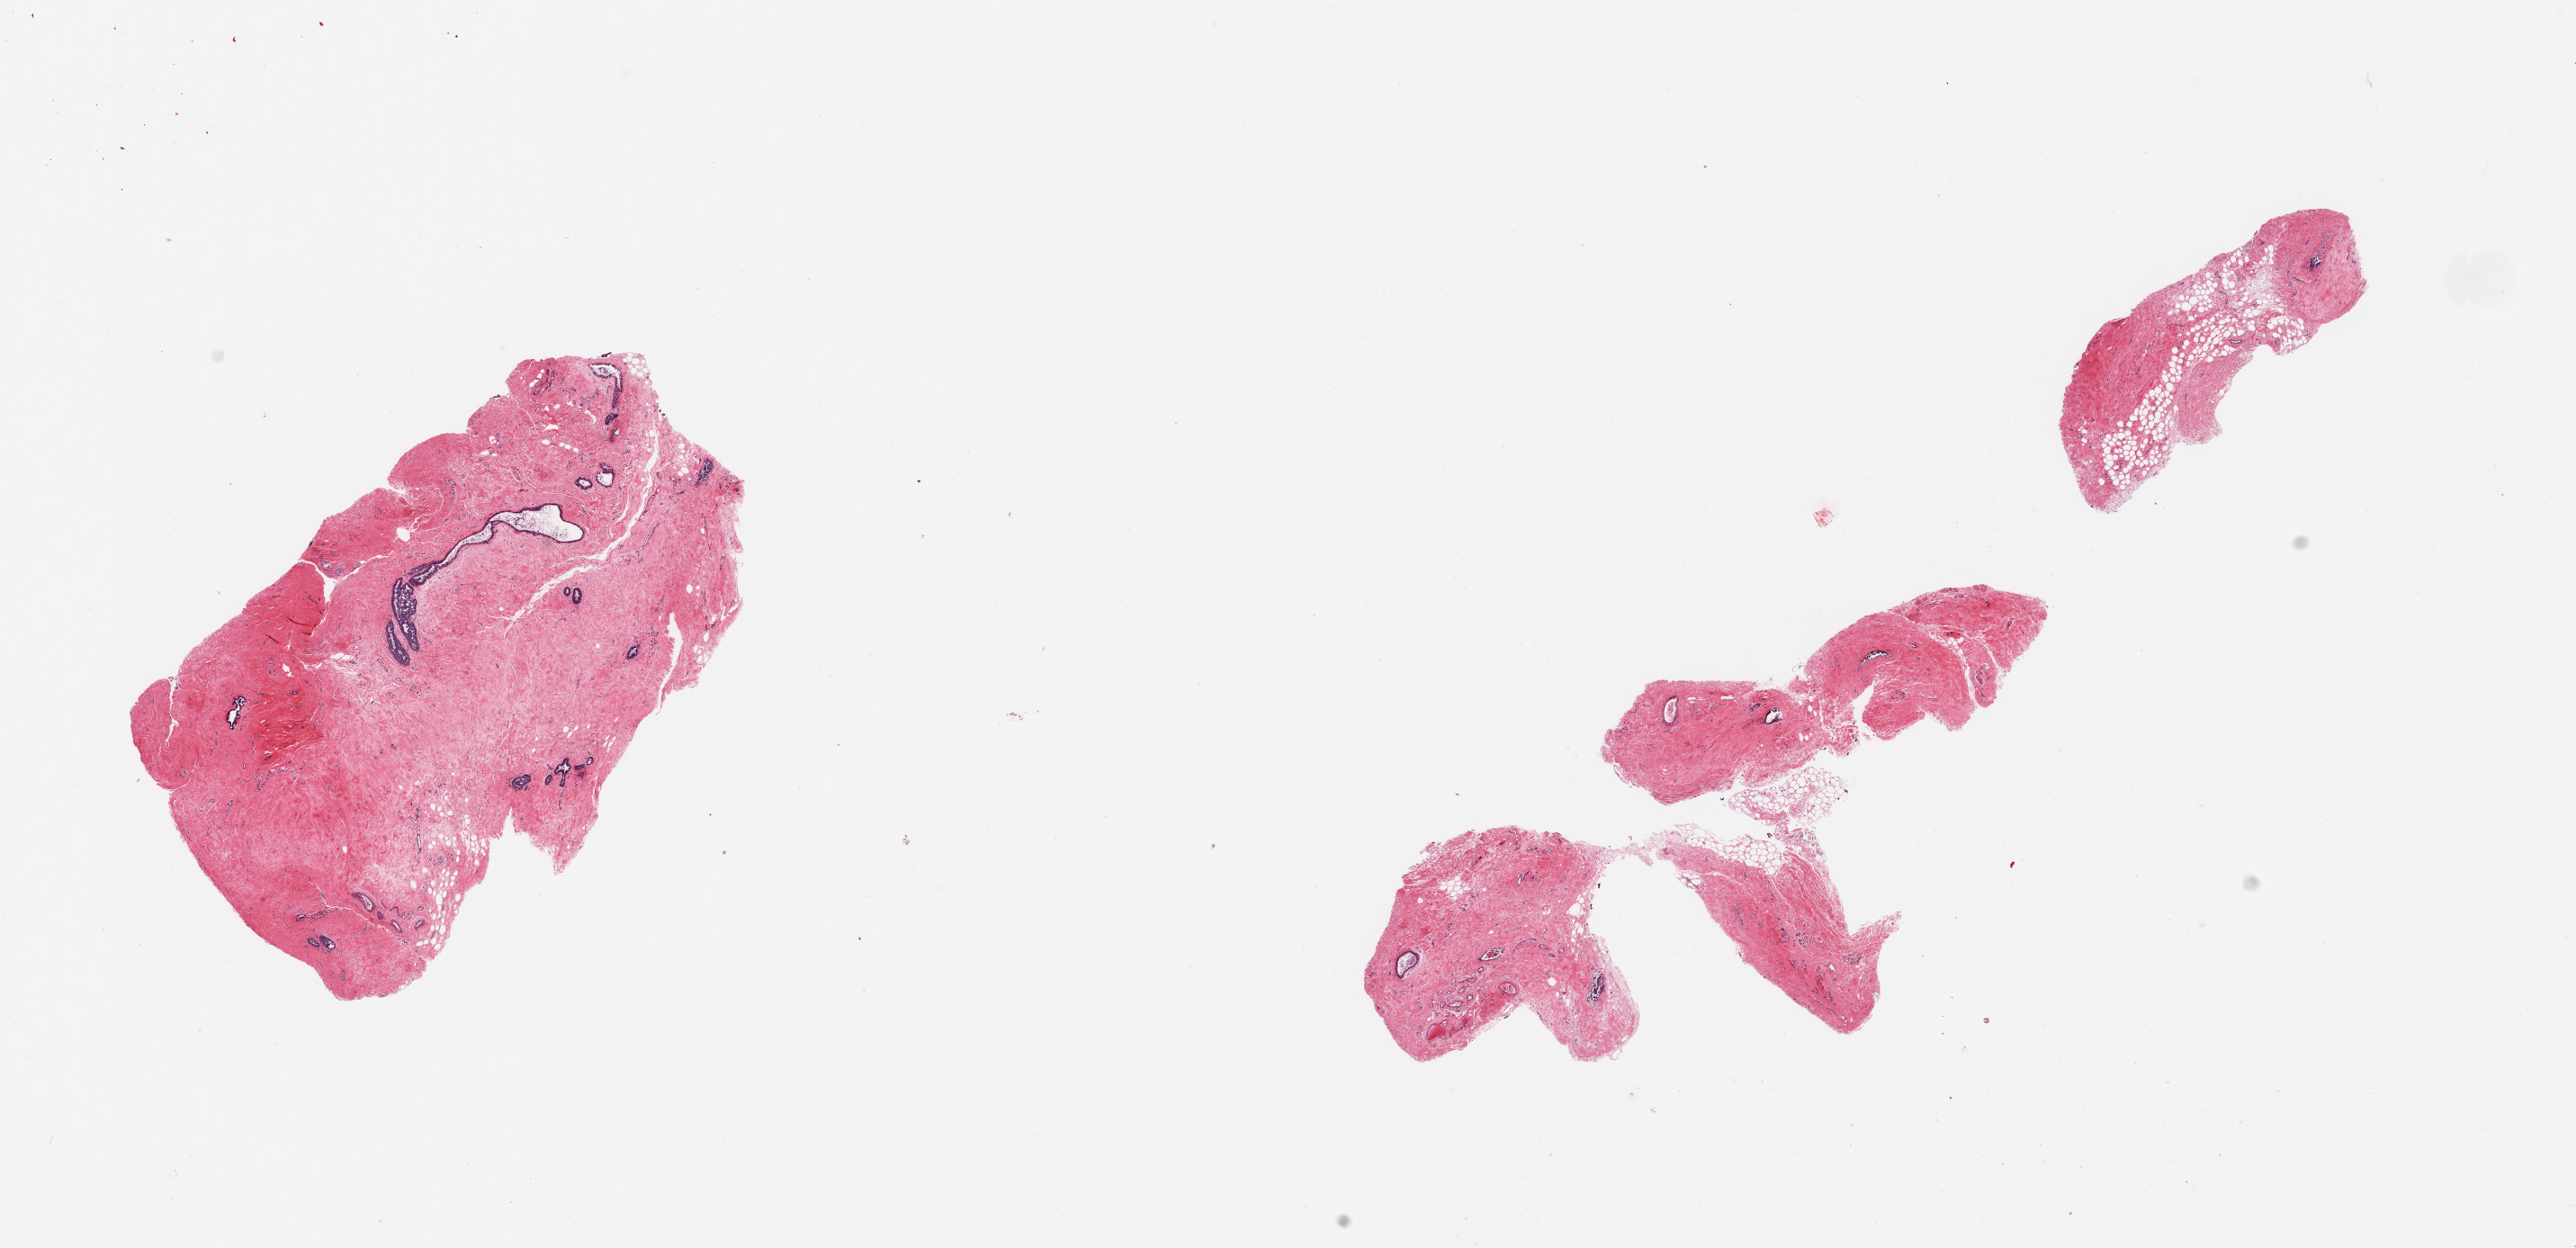
H&E whole-slide image, a low-resolution overview of the entire scanned area, about 22.6 x 11.0 mm (slide scanned at 20x), PAXgene-fixed paraffin-embedded (PFPE) section, target tissue: breast, tissue donor sample. Donor: male.
* review note (as recorded): 2 pieces; dense stroma with scattered ducts with some gynecomastoid features (hyperplastic)